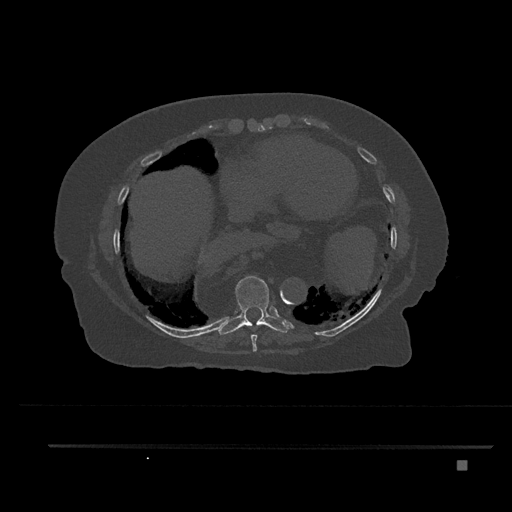
CT including the spine, one axial slice. Slice 410 of 797 in the series (ordered by position). Reconstruction kernel Br40s/3. Bone window (W 1800 / L 400 HU). 0.5 mm slice thickness. 512 × 512 image matrix, field of view 437 × 437 mm. Female patient, age 76 years. Case-level facts recorded for this patient, not image findings: primary cancer: lung; vertebrae with lytic lesions (as recorded): T11, L3.
Annotated regions visible in this slice (semi-automatically segmented with operator editing):
- T8 vertebra: bounding box <250,334,257,352> (left, top, right, bottom; pixels)
- T9 vertebra: <217,276,289,335>